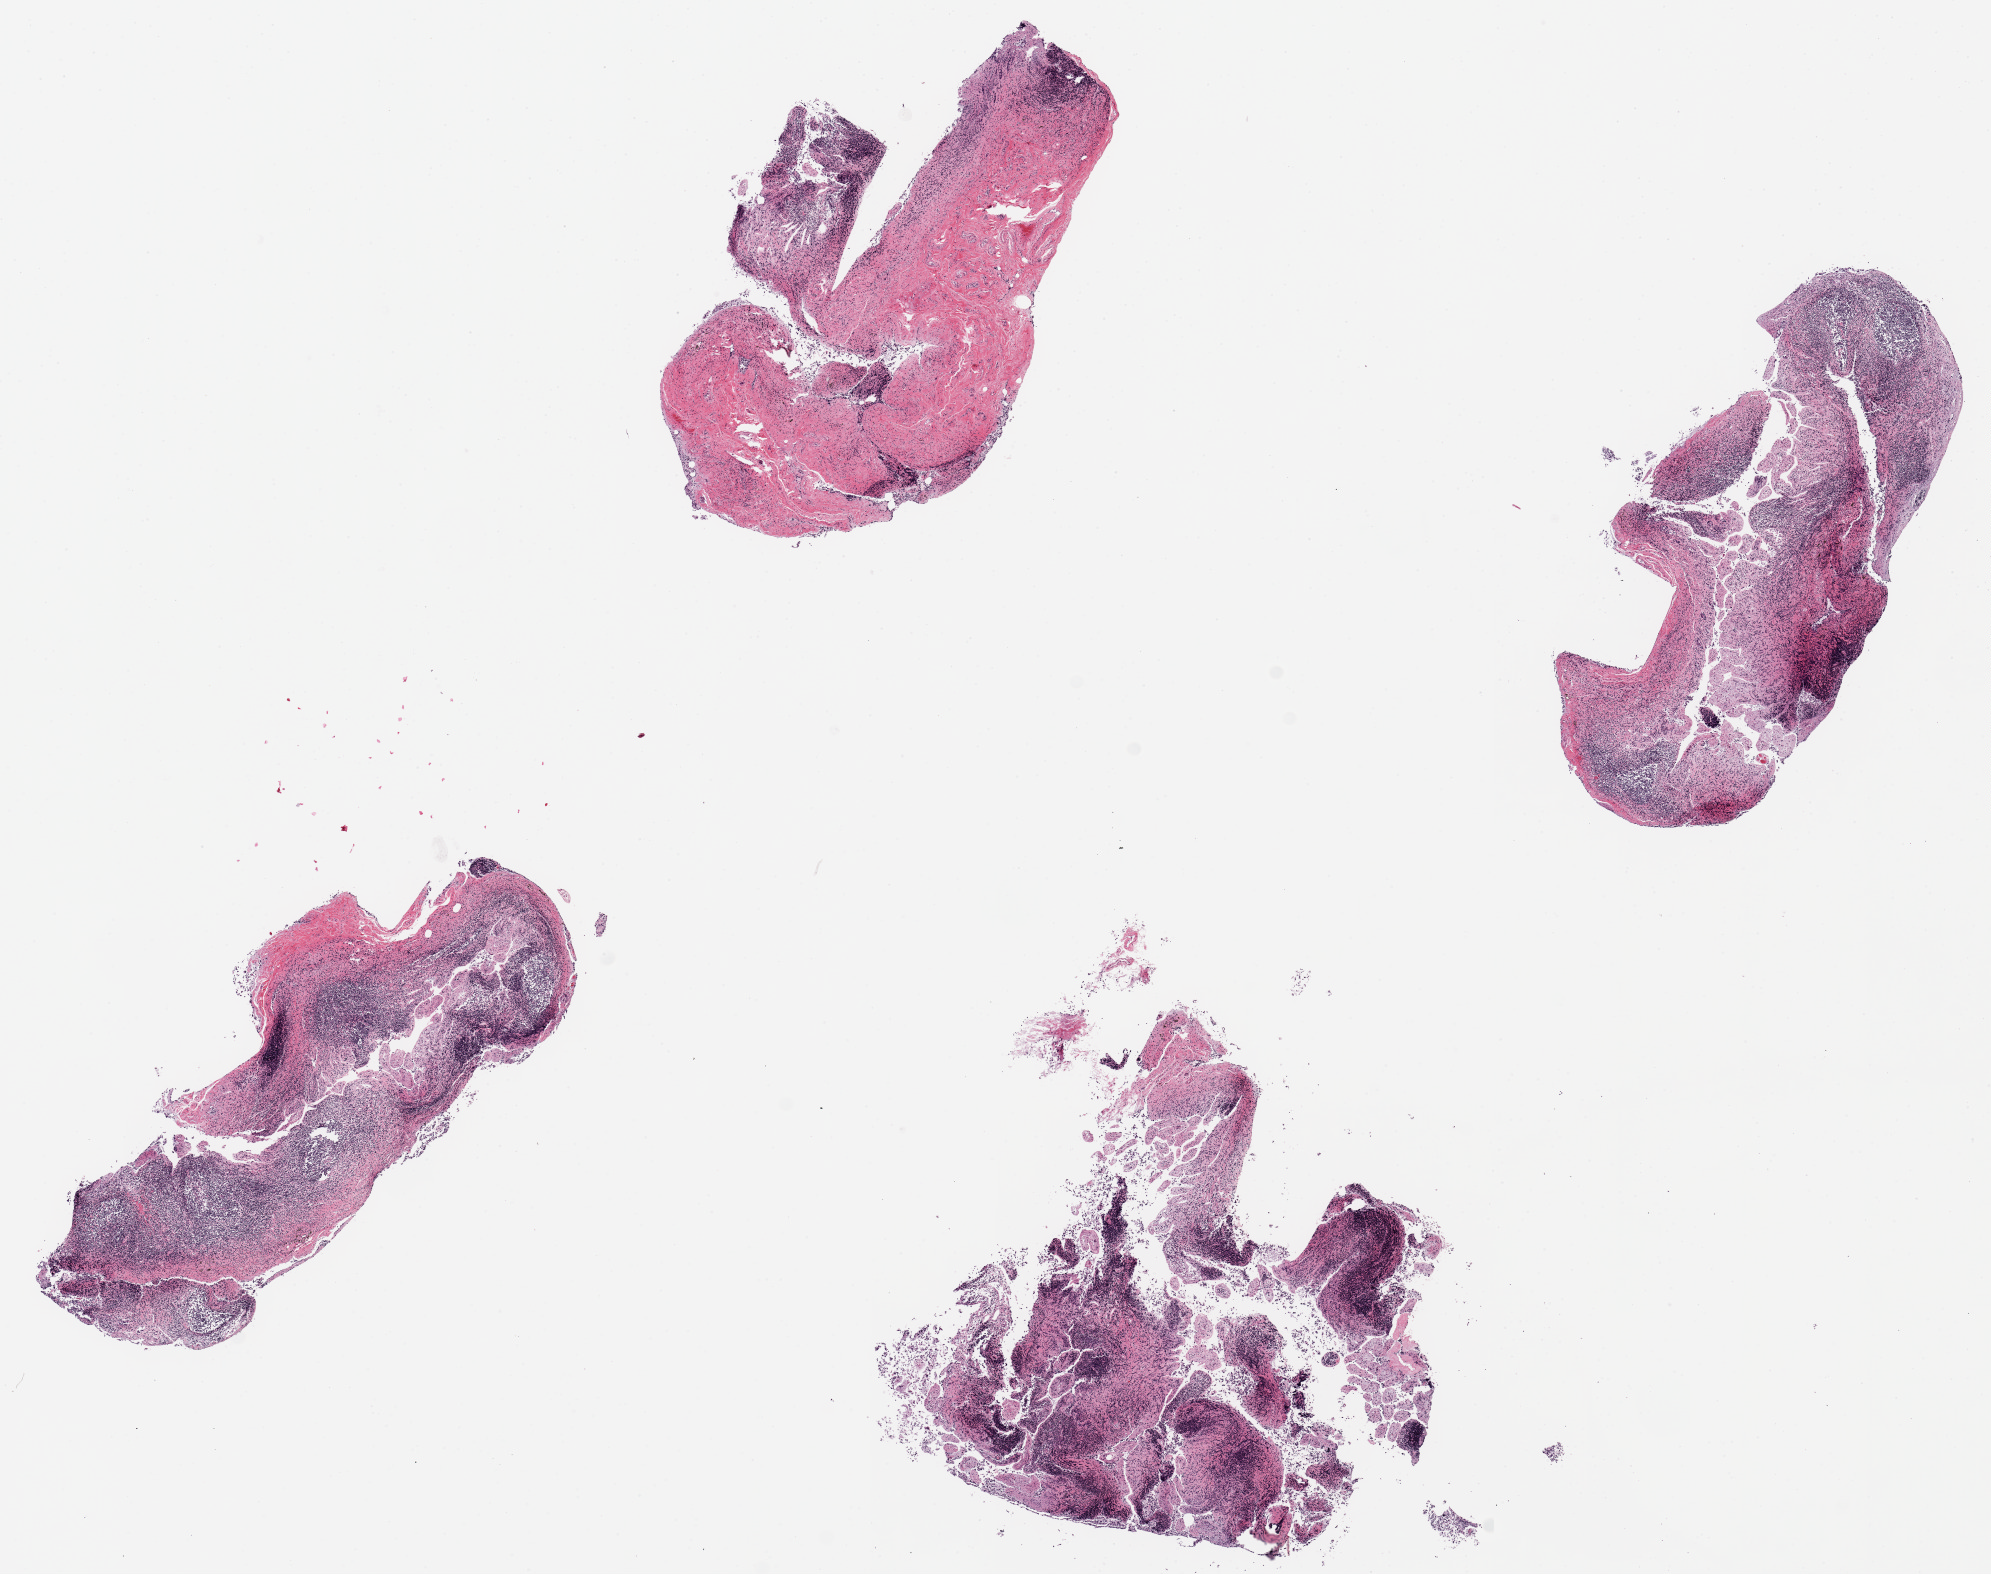
Digitized H&E-stained section, low-resolution overview of the scanned area, about 15.8 x 12.5 mm, PAXgene-fixed, paraffin-embedded tissue, target tissue: ileum, donor tissue sample. Donor sex: female.
Review note (as recorded): 4 pieces, up to 5.5x5mm; numerous lymphoid nodules (good) (=2); mucosa =3.